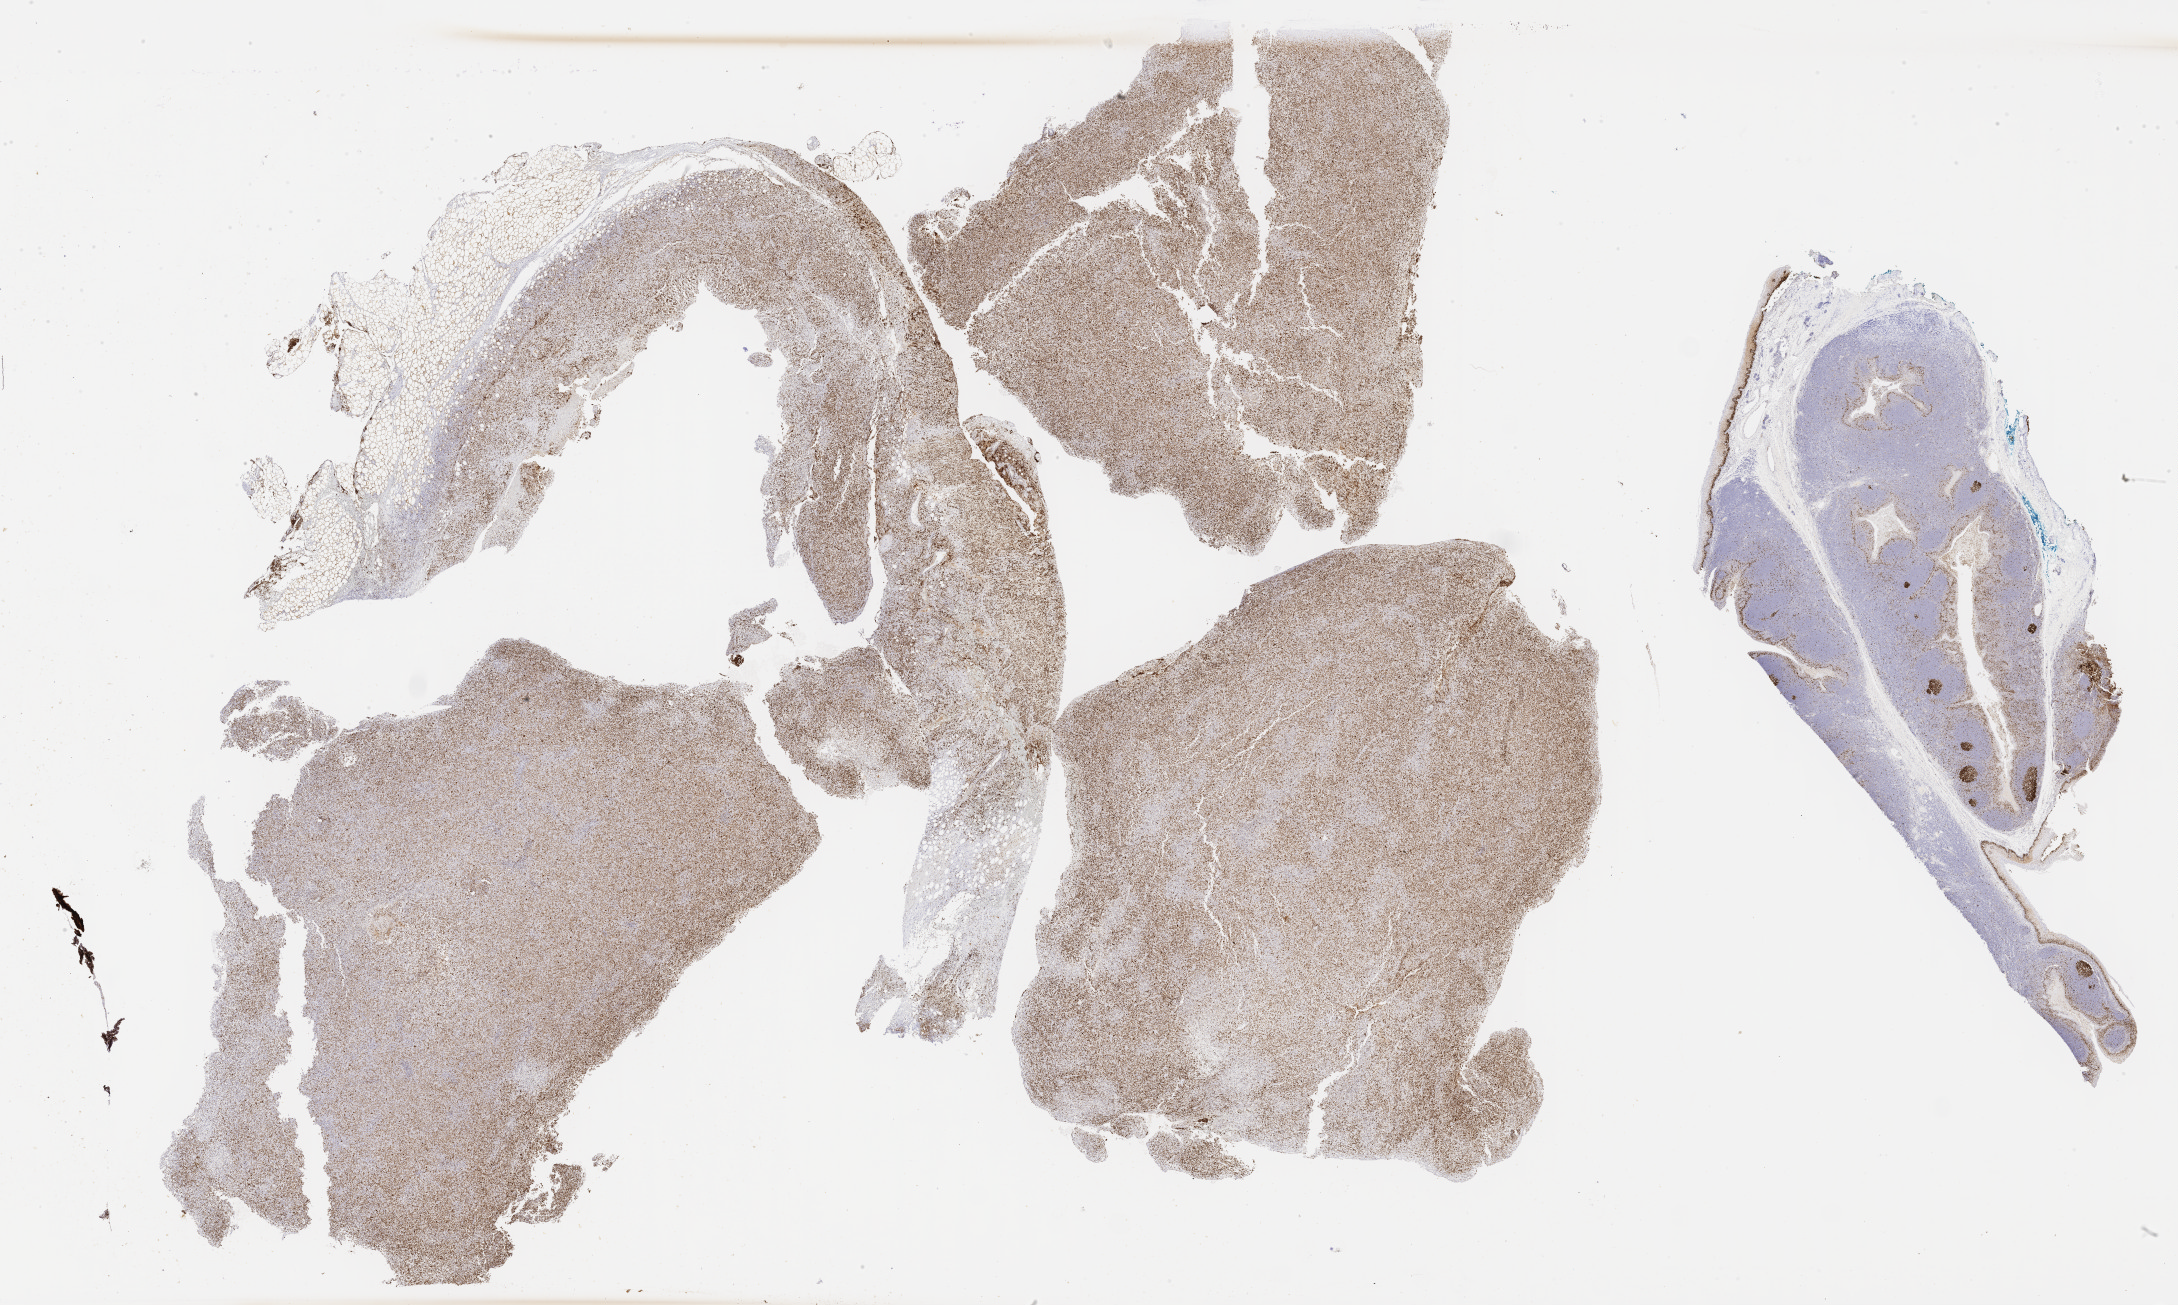
IHC for Ki-67, whole-slide image — low-resolution overview of the scanned area, about 35.2 x 21.1 mm. Patient sex: female.
Specimen: tumor tissue.